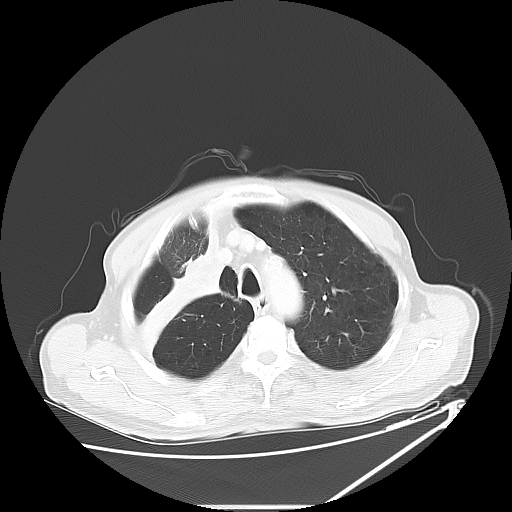
Chest CT, one axial slice. Position 49 of 60 along the scan axis. 120 kVp. Lung window (W 1500 / L -600 HU). 512 × 512 image matrix, field of view 410 × 410 mm. Male patient, age 73 years. From the clinical record (not read from this slice): clinical TNM (as recorded): T2a N1 M0.
Structures marked on this image (bounding box drawn by a radiologist):
- lung tumour (recorded histology: squamous cell carcinoma): bounding box (x1, y1, x2, y2) in pixels: (130, 237, 231, 368)